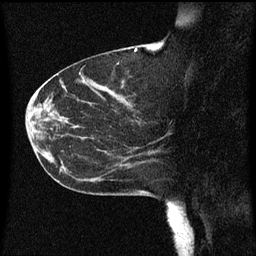
Breast MRI (dynamic contrast-enhanced), one sagittal slice; dynamic contrast-enhanced series, image 2 of 3 at this slice position (ordered by acquisition); 1.5 T; TE 4.2 ms, TR 8 ms; 2 mm slice thickness; 256 × 256 image matrix, field of view 200 × 200 mm. Female patient, age 55 years.
Structures marked on this image (semi-automatic segmentation, software-assisted and operator-edited):
- analysis volume of interest (the breast-tissue region the enhancement analysis was run in; not a lesion): bounding box [x1, y1, x2, y2] px = [46, 124, 151, 183]
- tumour enhancement mask (voxels above the 70 % enhancement threshold inside the analysis volume of interest): [134, 148, 143, 165]